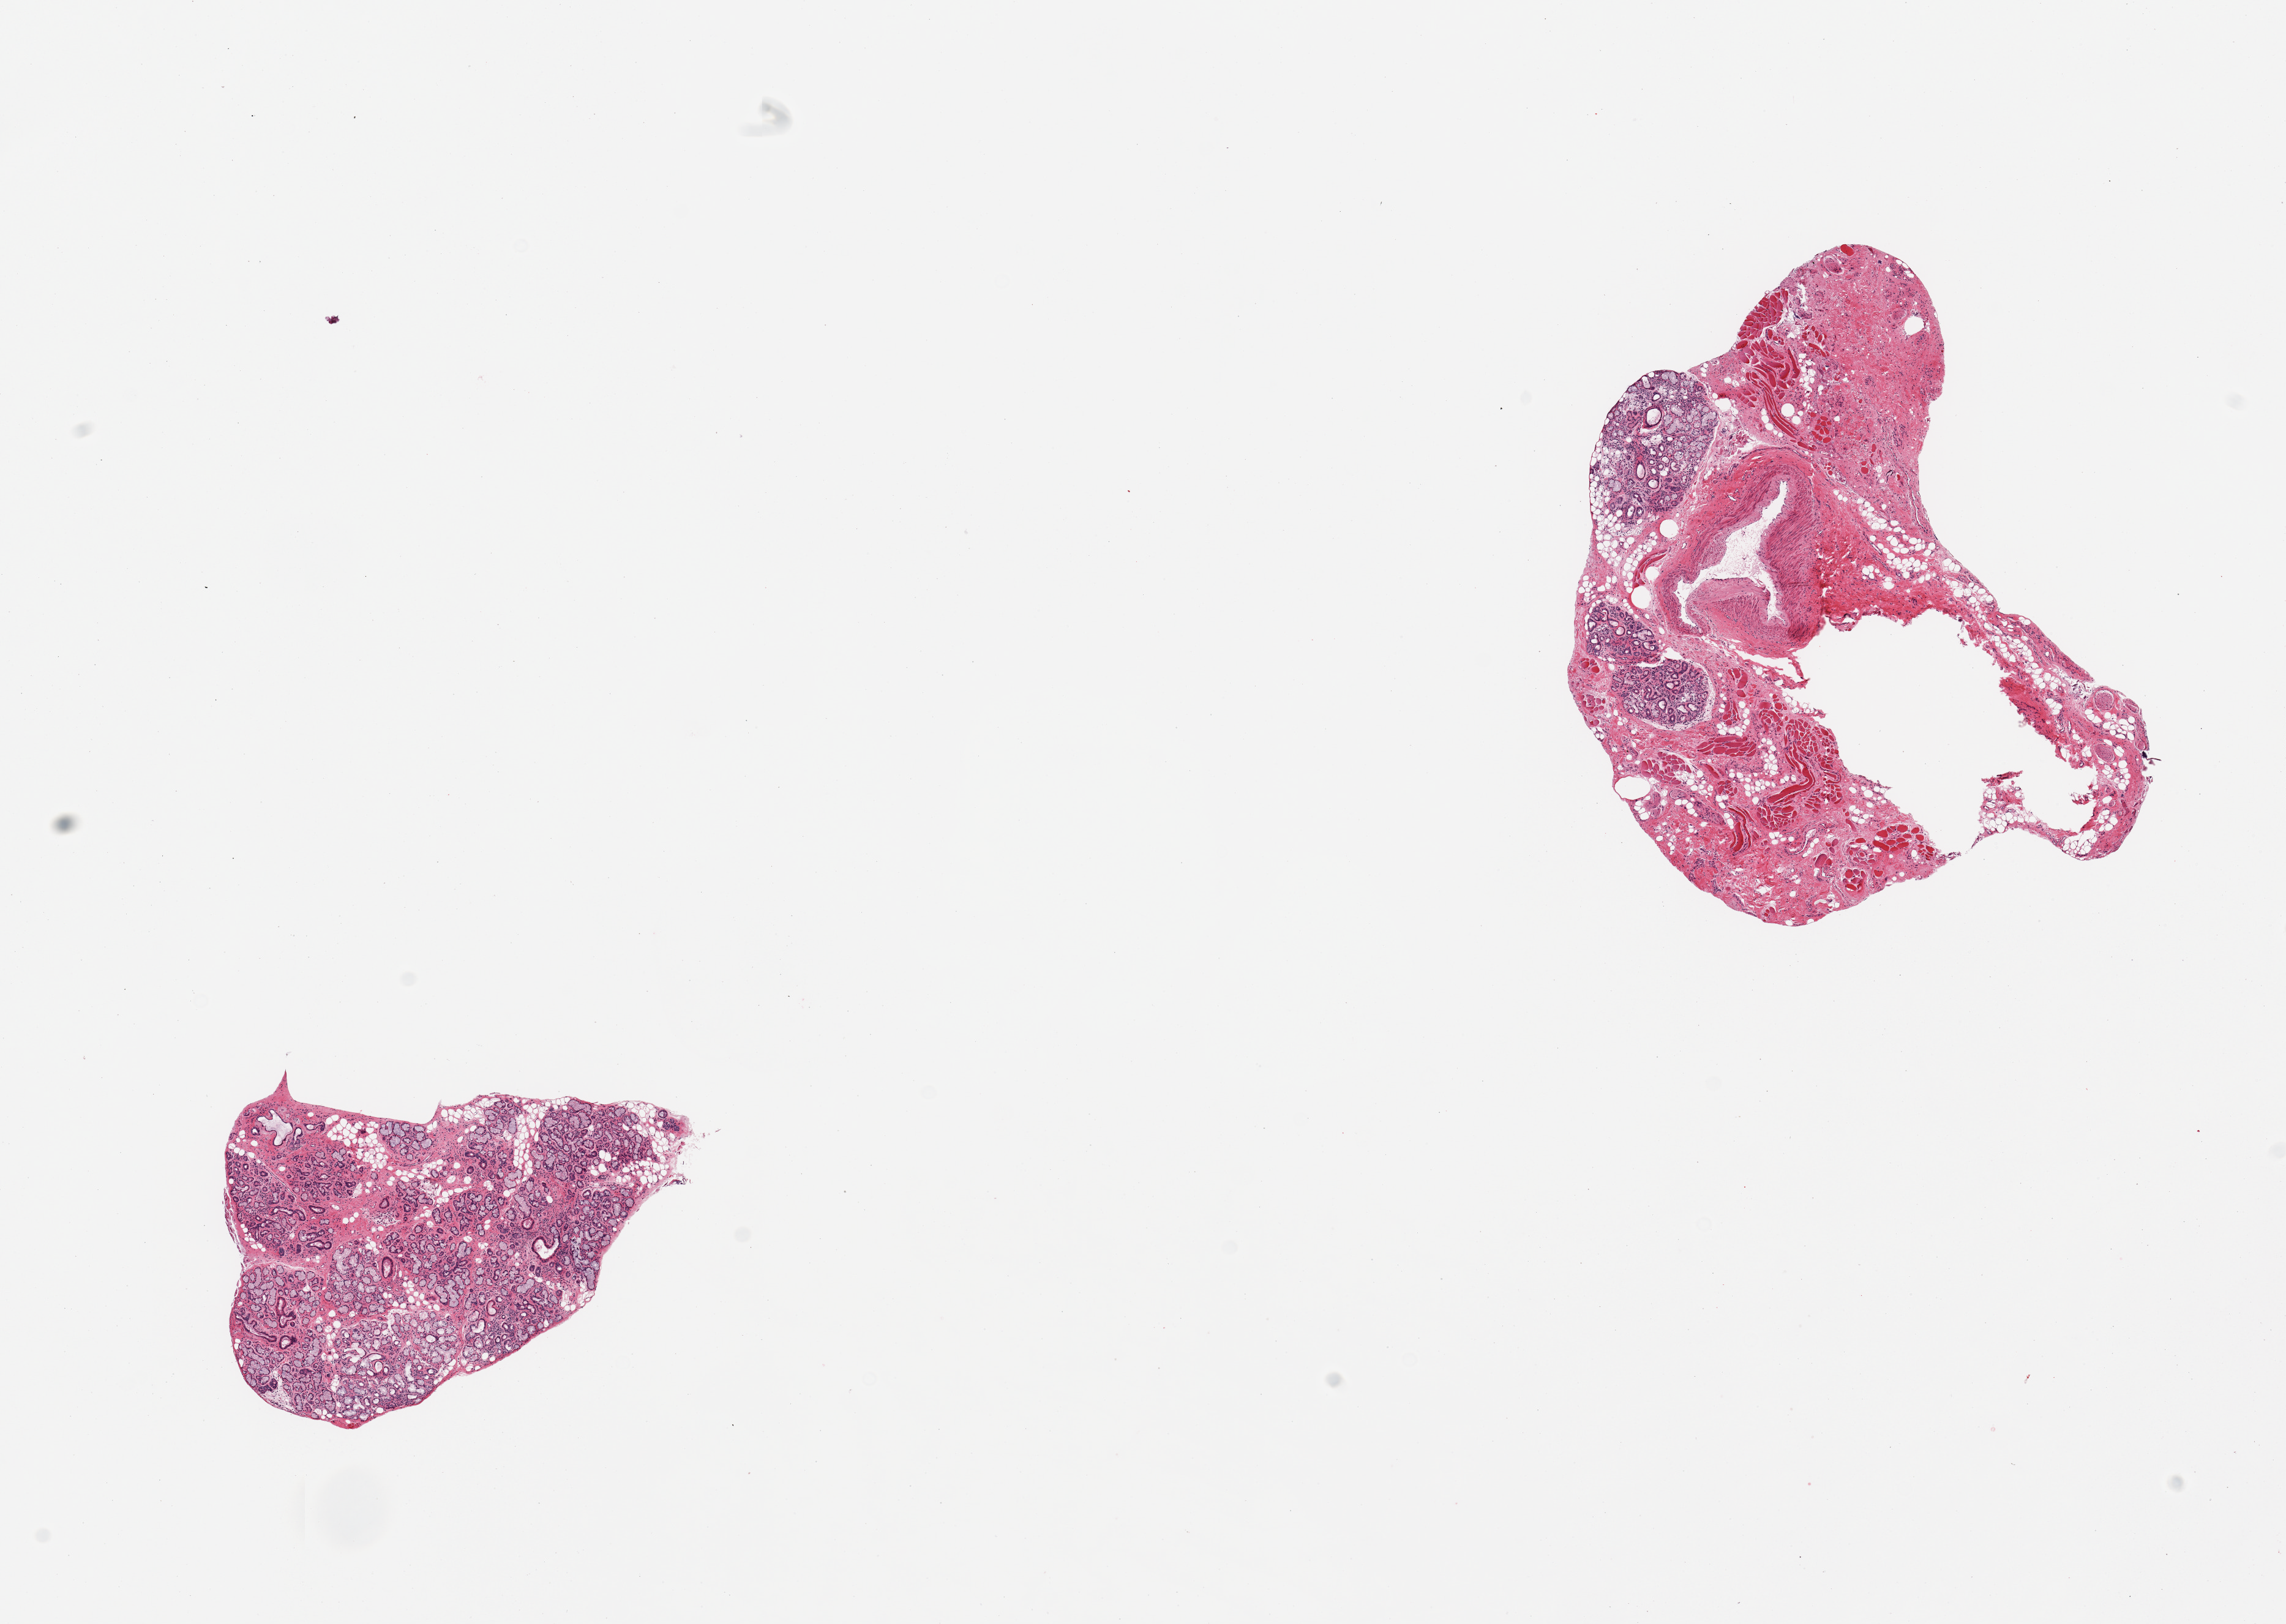
Digitized haematoxylin and eosin-stained section, brightfield, whole scanned area (about 14.8 x 10.5 mm, slide scanned at 20x) shown as a low-resolution overview. PAXgene-fixed paraffin-embedded (PFPE) section. Target tissue: minor salivary gland. Donor tissue sample. Male donor.
Reviewer comment on this tissue sample: 2 pieces, ~50% target glandular elements.